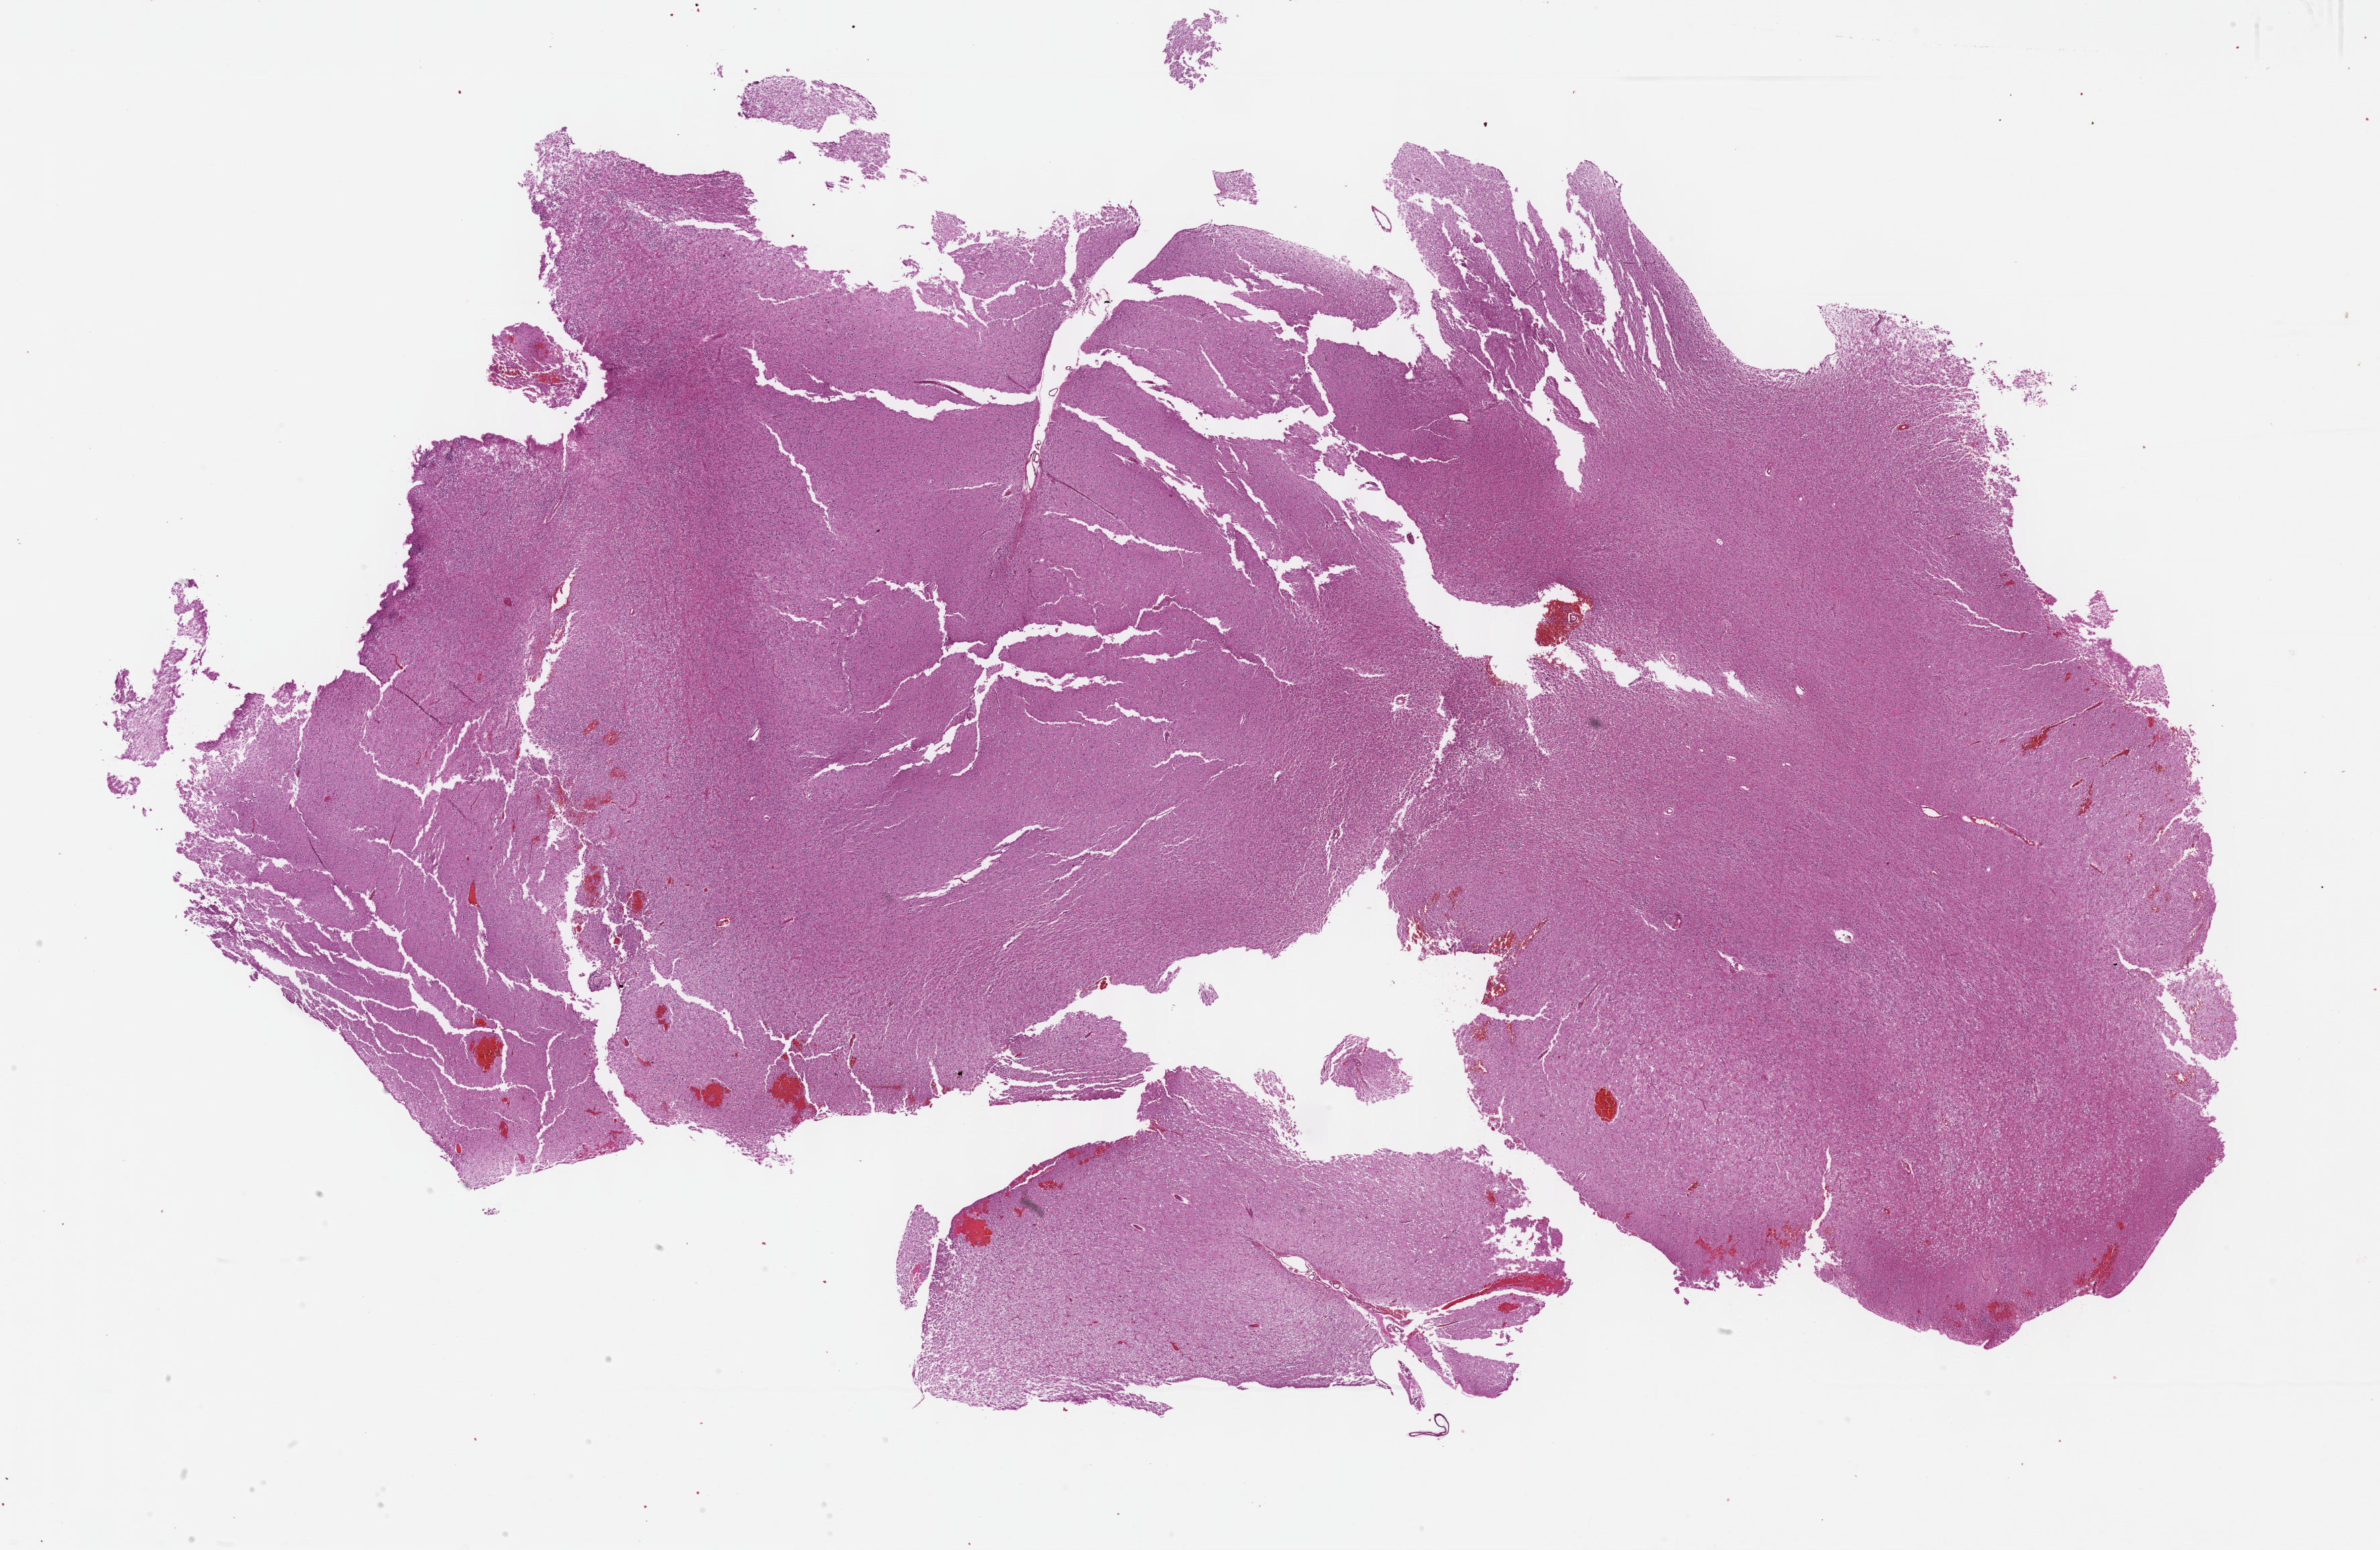
Digitized Hematoxylin and eosin (H&E) stained tissue section (whole slide) — a low-resolution overview of the entire scanned area, about 28.7 x 18.7 mm; formalin-fixed paraffin-embedded (FFPE) diagnostic section; primary tumour sample from the brain. Female, age 48 years at initial diagnosis. Histologic grade: G2 (moderately differentiated).
Laterality: left. Pathologic diagnosis: Mixed glioma.